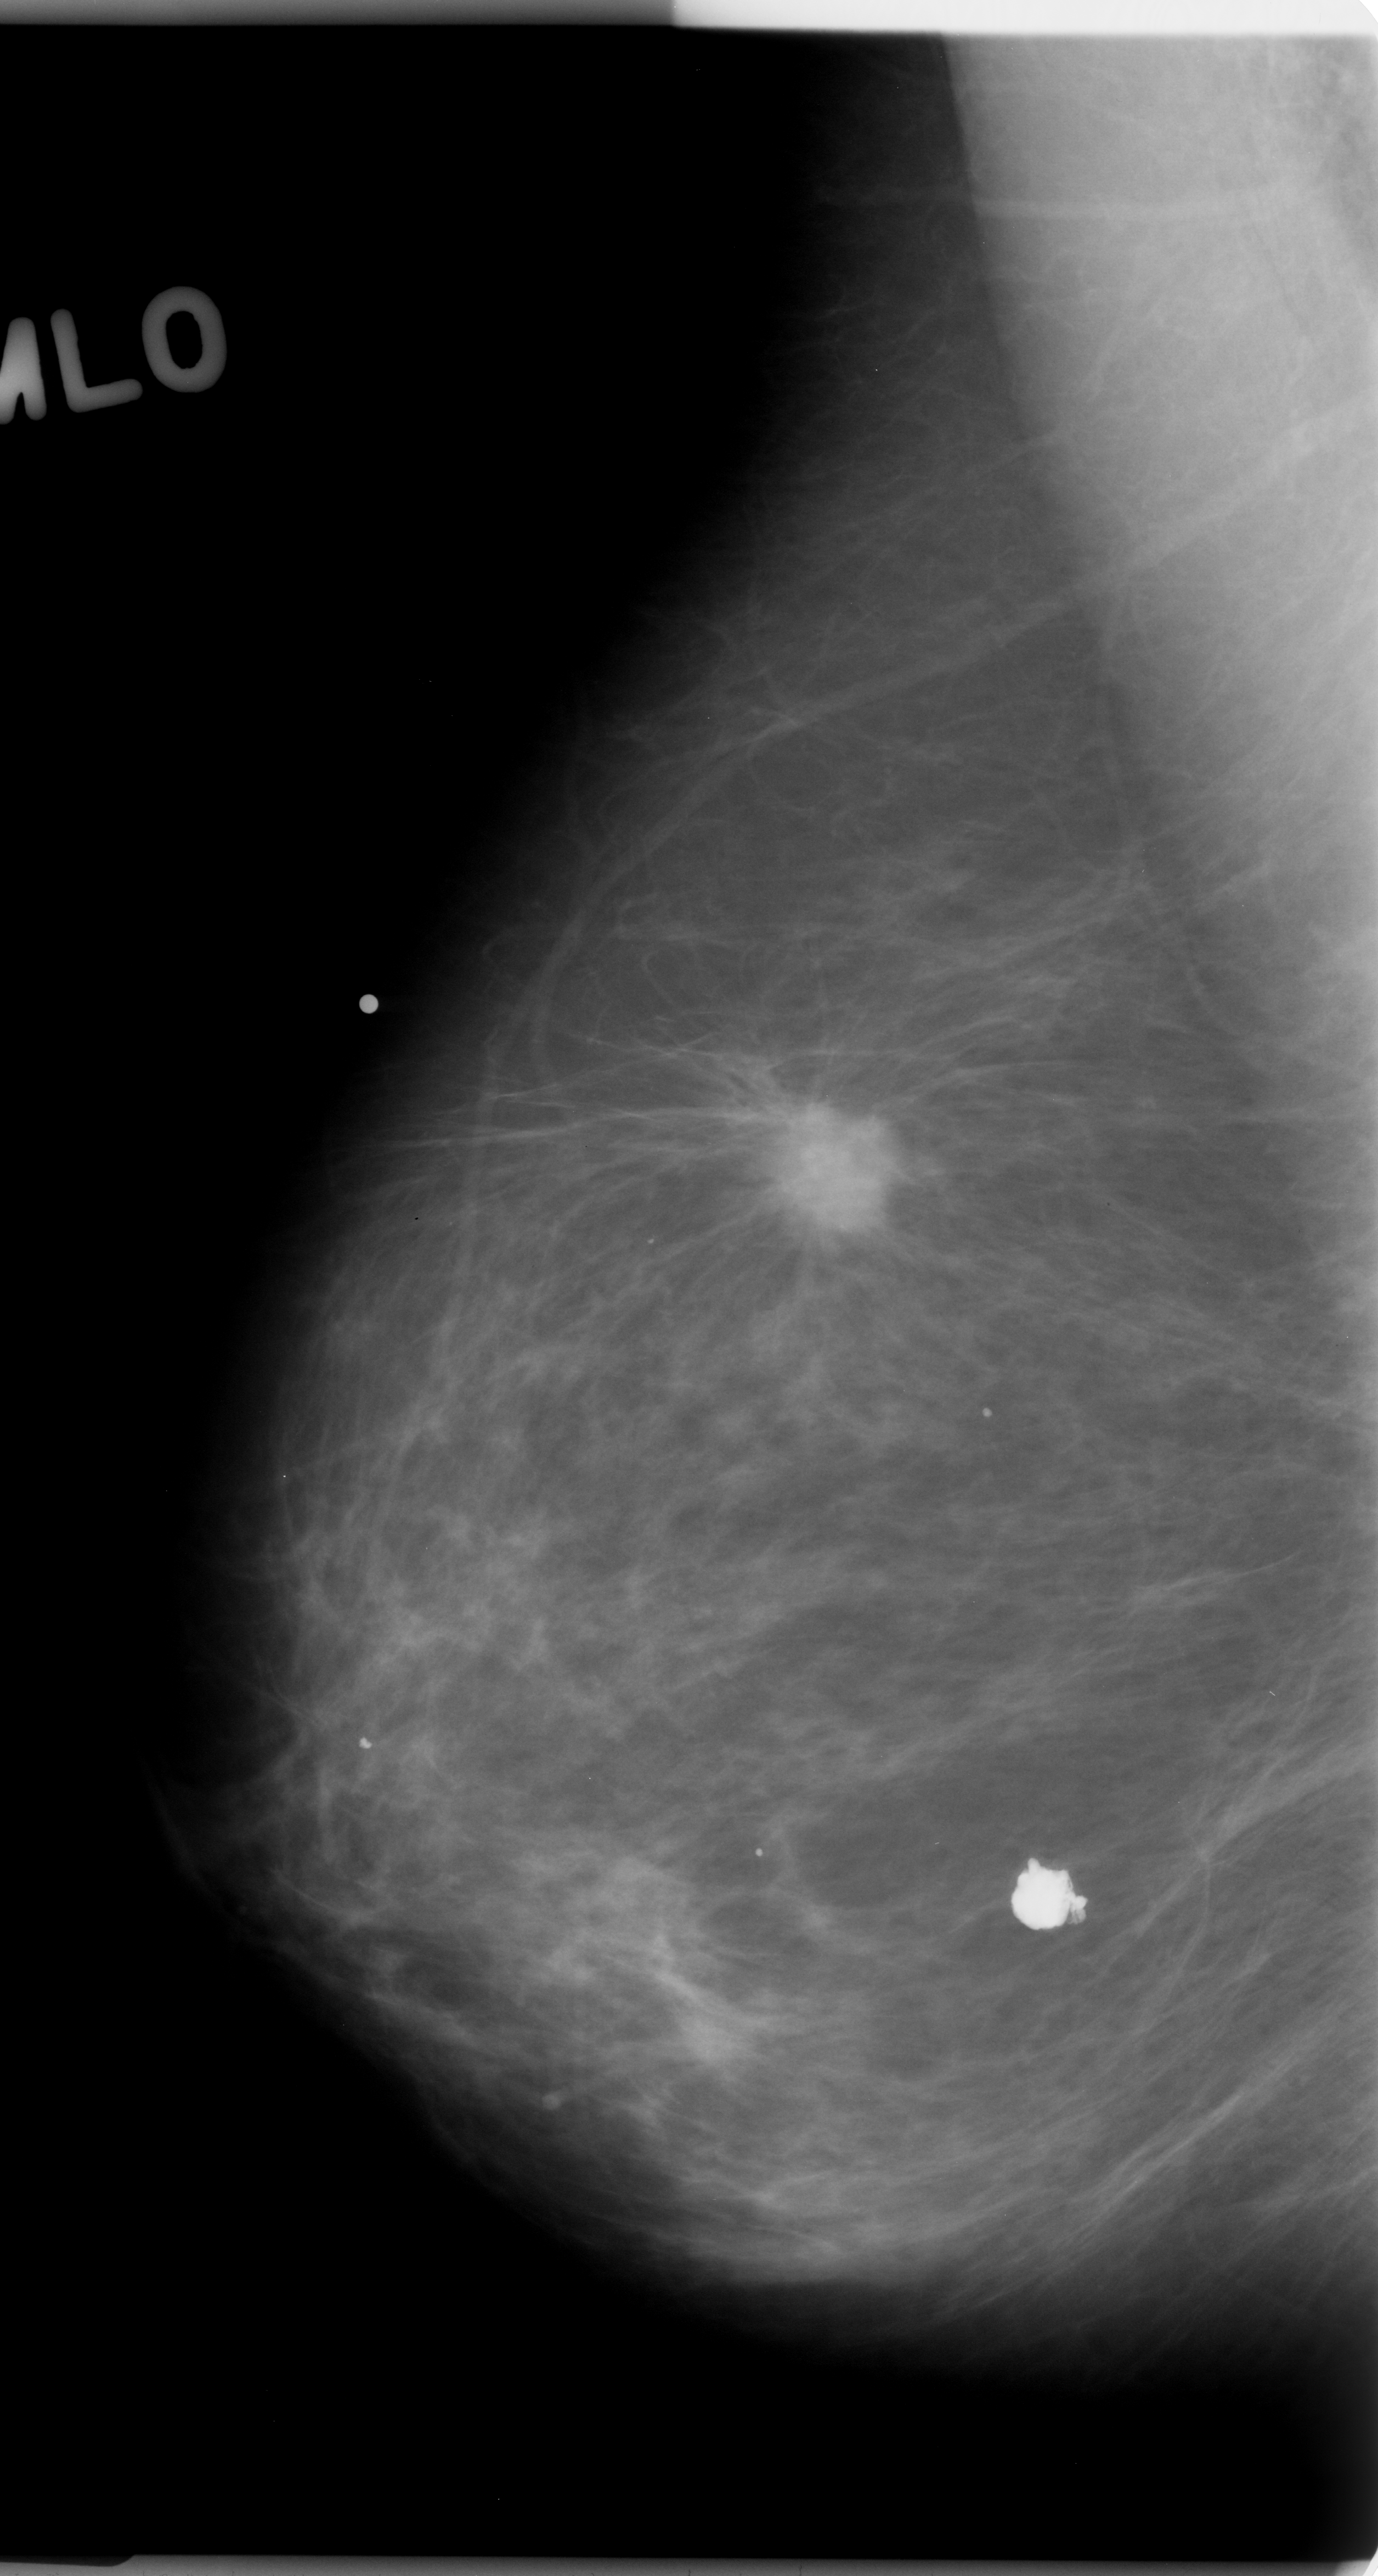
Mammogram (digitized film); right breast; MLO view; BI-RADS breast density category 1 (scale 1–4); 1378 × 2576 image matrix.
Marked abnormalities (boxes around the expert regions of interest):
- mass, shape irregular, margins spiculated; BI-RADS assessment category 5; pathology result (as recorded, not read from the image): malignant: bounding box [x1, y1, x2, y2] px = [733, 1077, 912, 1239]